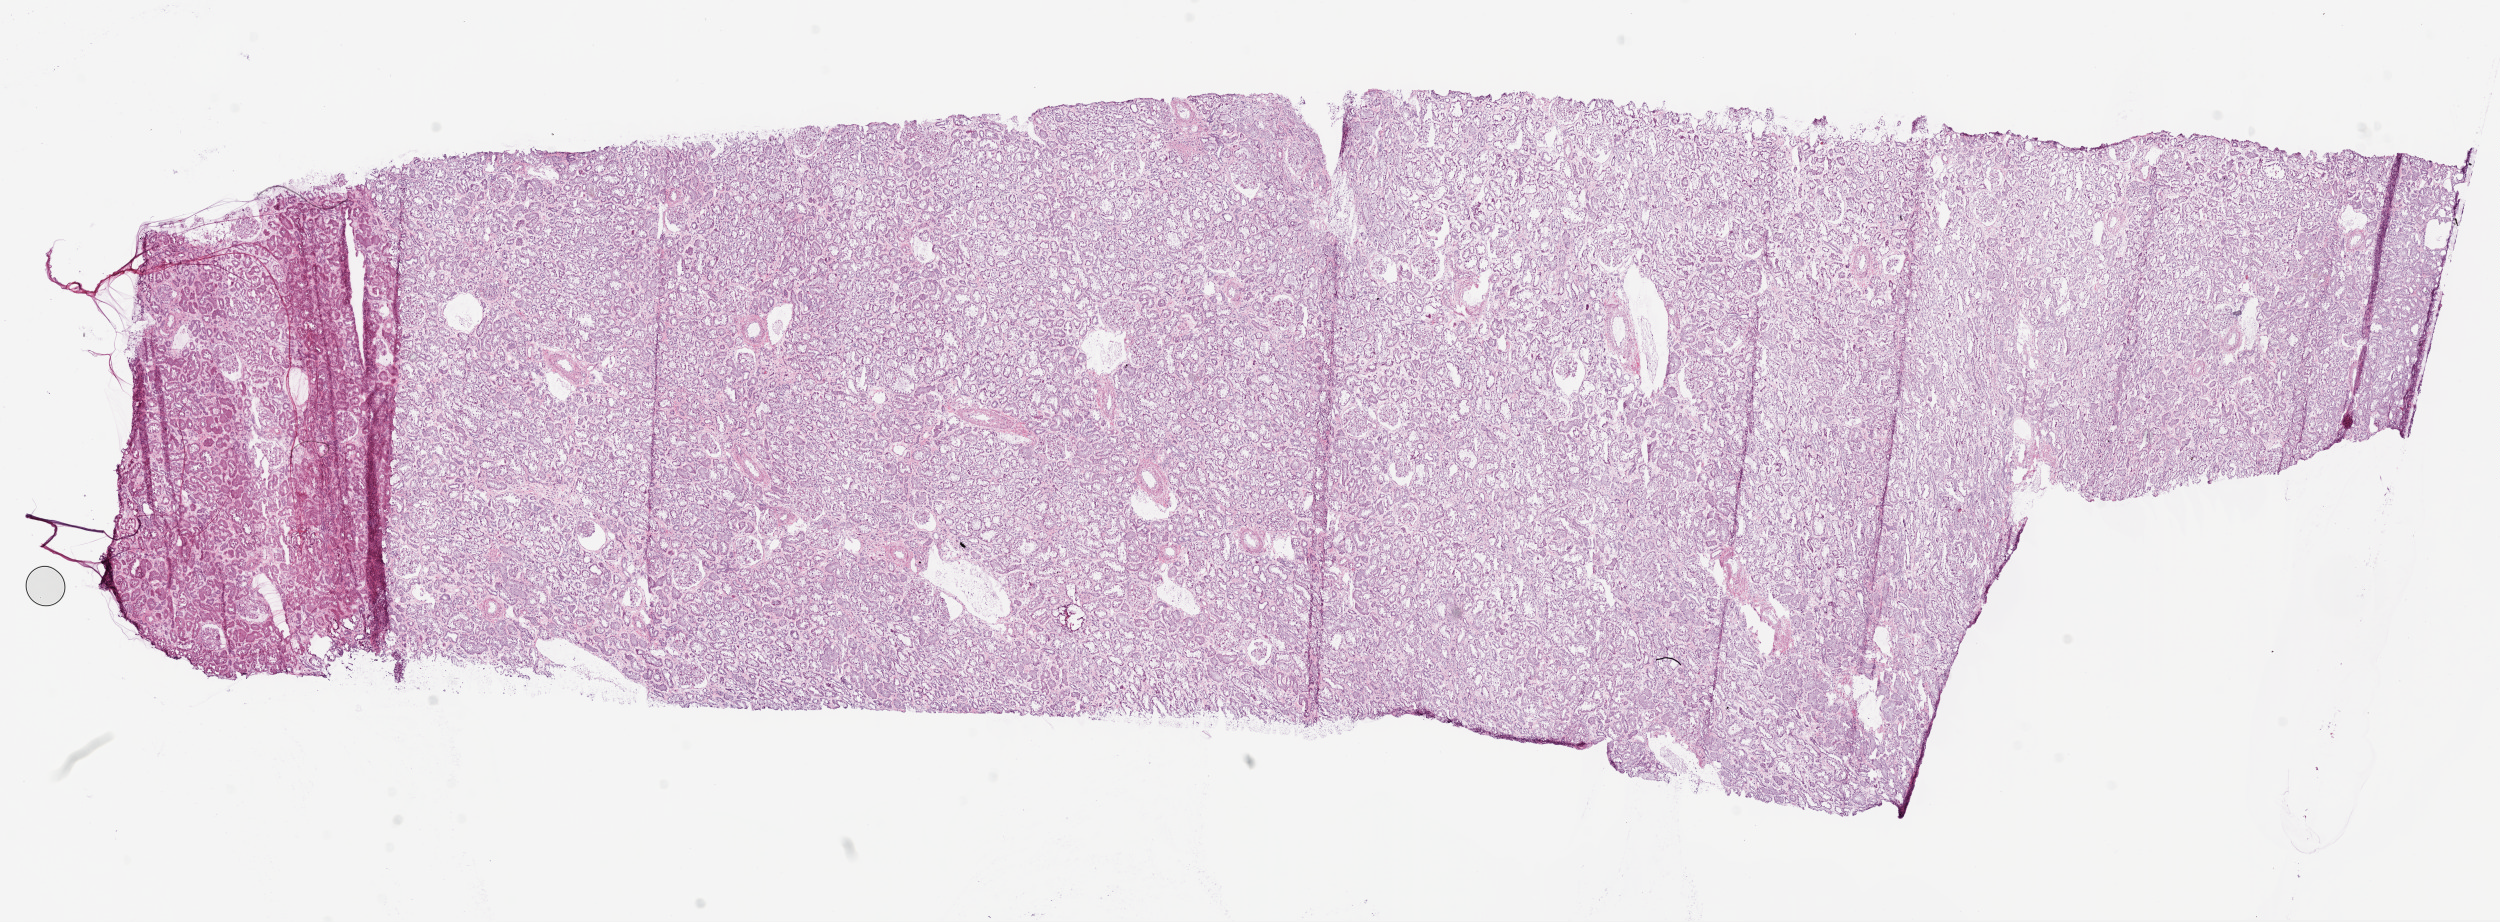
Hematoxylin and eosin (H&E) stained whole-slide image — shown as a low-resolution overview of the whole scanned area (about 20.1 x 7.4 mm, from a 20x scan). Frozen section from the top of the tissue portion. Kidney, solid tissue normal (non-tumour tissue) sample. Male, age 52 years at initial diagnosis.
This section: solid tissue normal sample (biorepository sample class). Patient diagnosis: Clear cell adenocarcinoma, NOS.